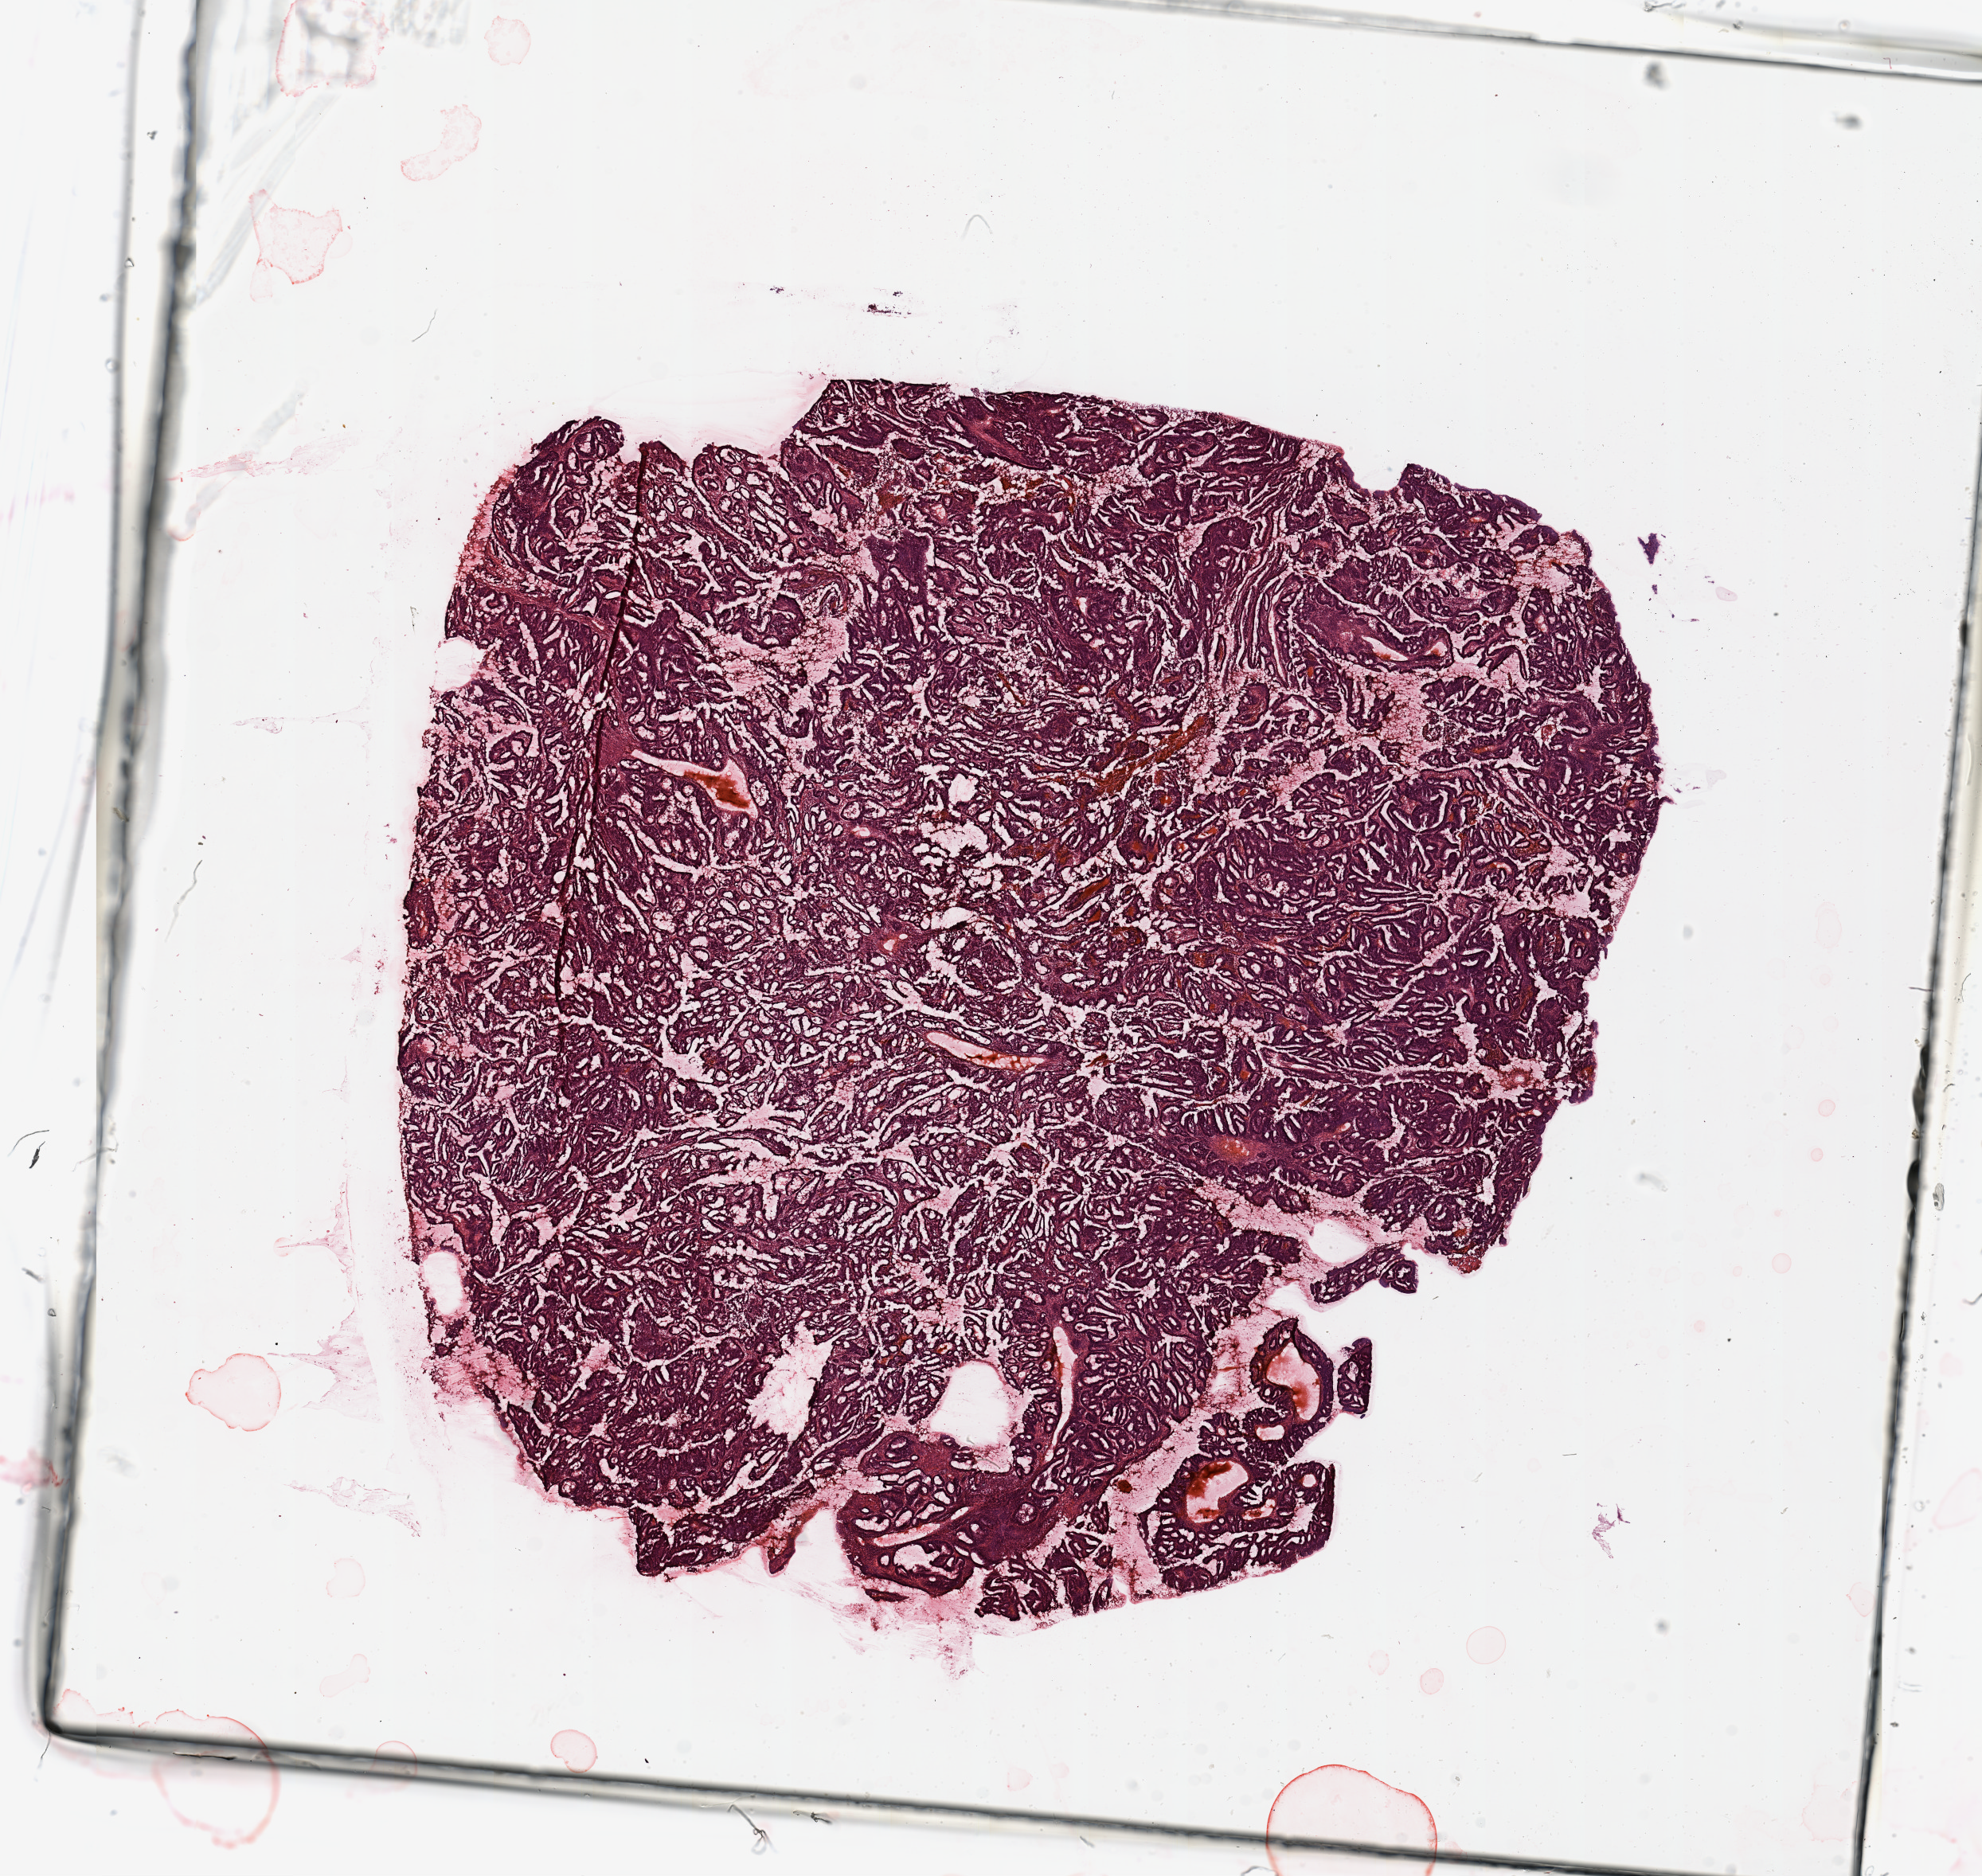
Hematoxylin and eosin (H&E) stained whole-slide image, whole scanned area (about 19.7 x 18.6 mm) shown as a low-resolution overview. Tumour tissue sample, uterus. Patient: female, age 65 years. Histologic grade: G2 (moderately differentiated).
Histologic diagnosis: Endometrioid adenocarcinoma, NOS. AJCC pathologic stage: III.